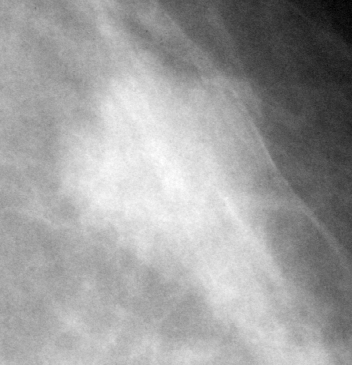
Region of interest cut from a scanned film mammogram (one marked finding), left breast, MLO view.
Finding: mass, shape lobulated, margins microlobulated; BI-RADS assessment category 4; subtlety rating 5 on a 1 (subtle) to 5 (obvious) scale; pathology result (as recorded, not read from the image): malignant.